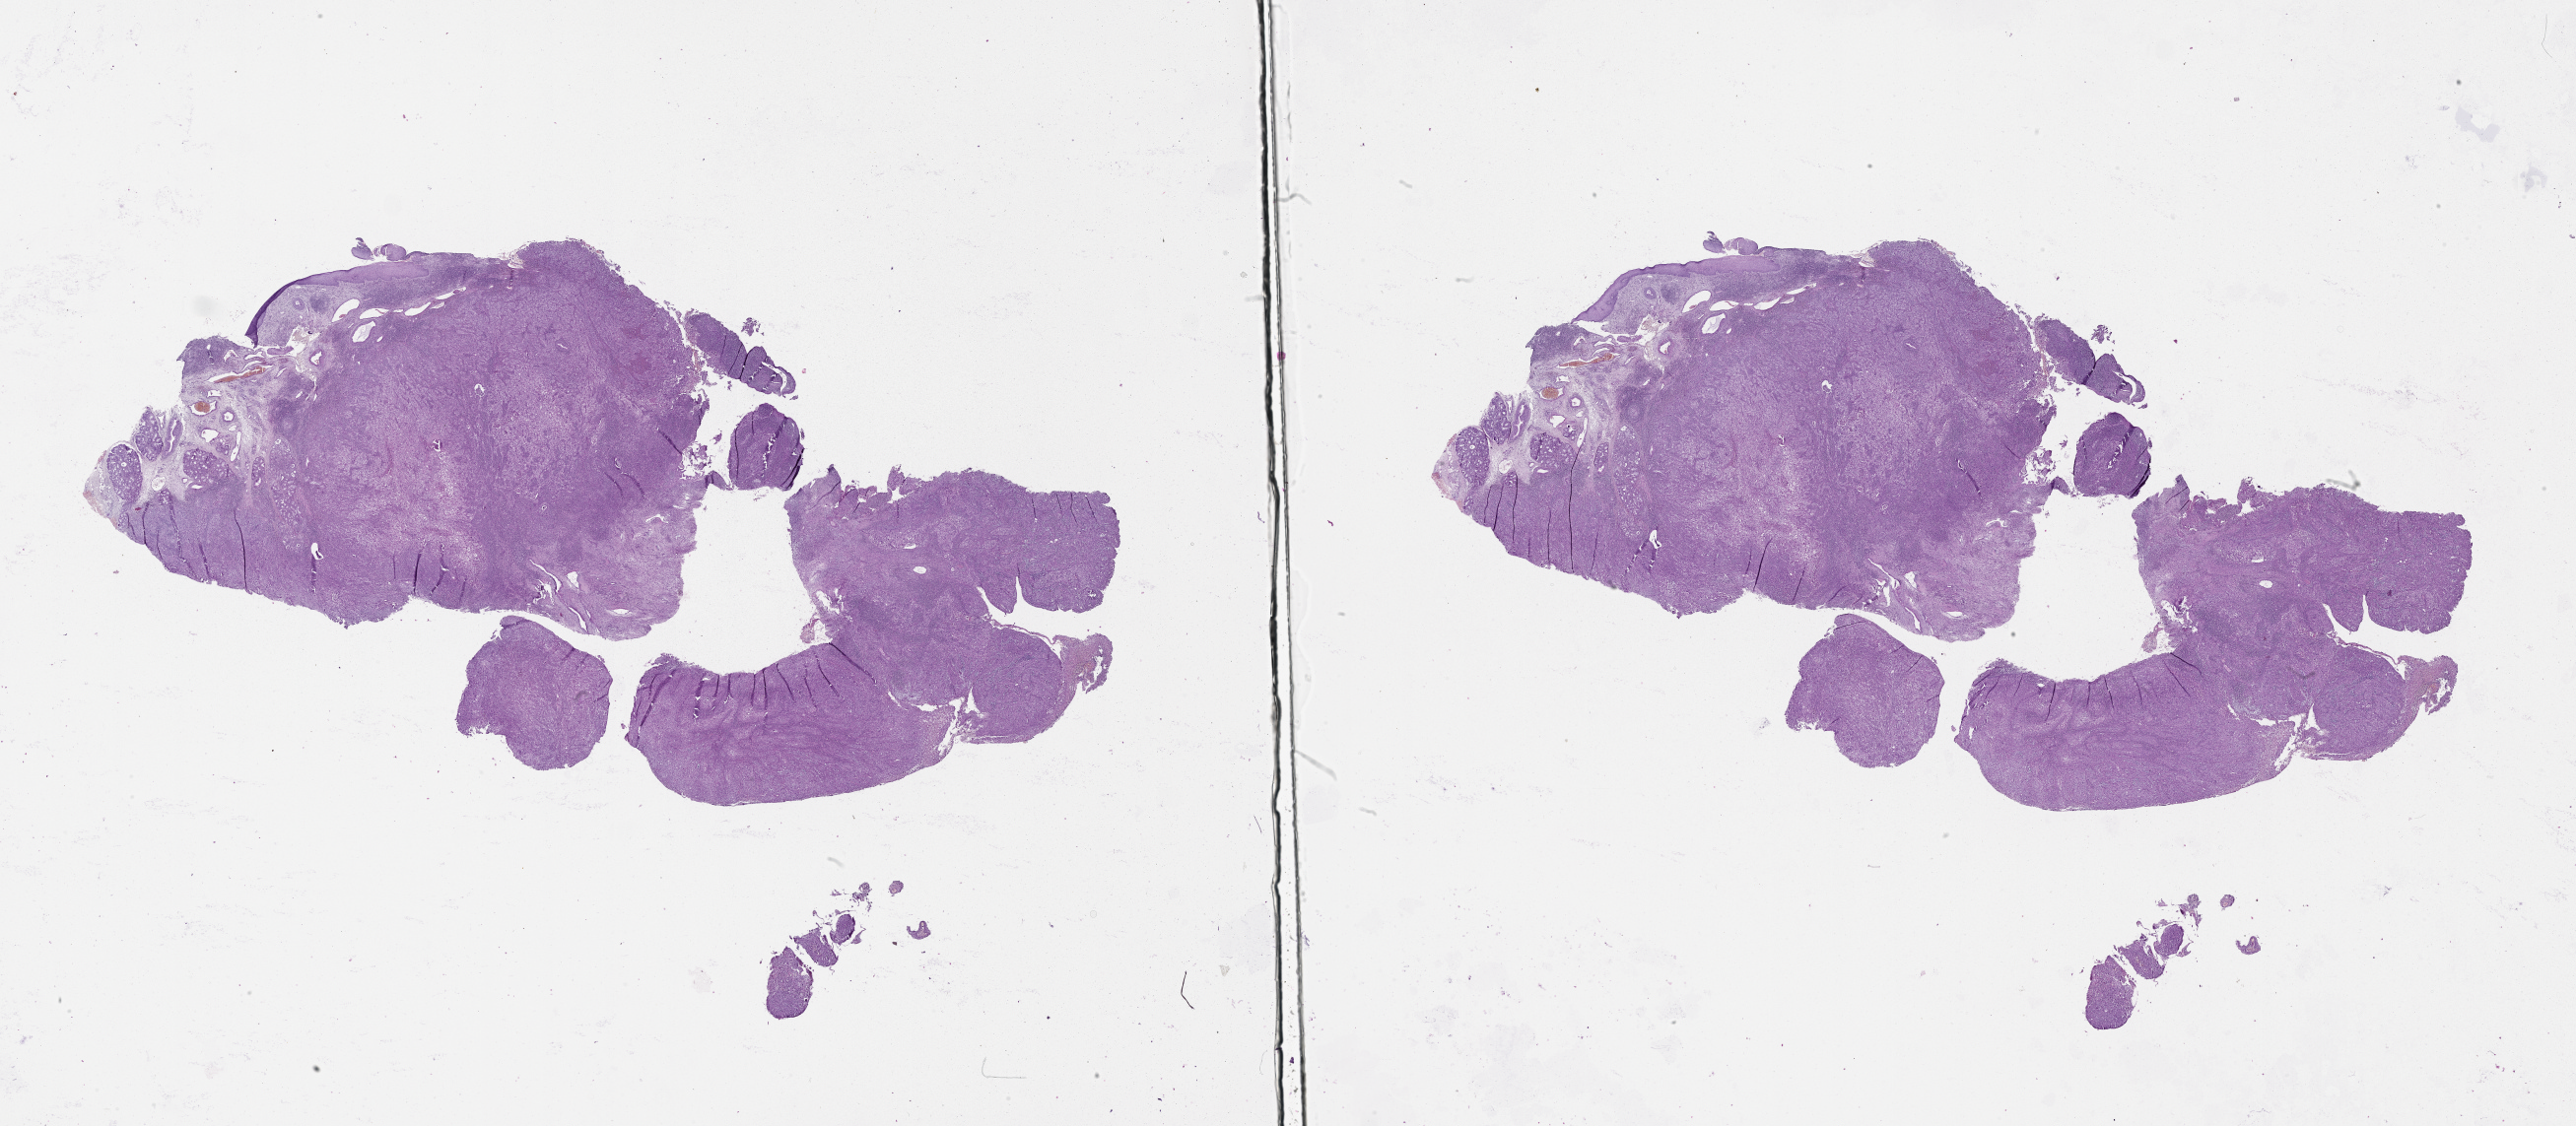
Whole-slide histology image, Hematoxylin and eosin (H&E) stained — low-resolution overview of the scanned area, about 42.1 x 18.4 mm (acquisition: 20x scan). Head and neck, tissue type not recorded. Male, 55 y/o.
Patient diagnosis: Squamous cell carcinoma, NOS (larynx, NOS).